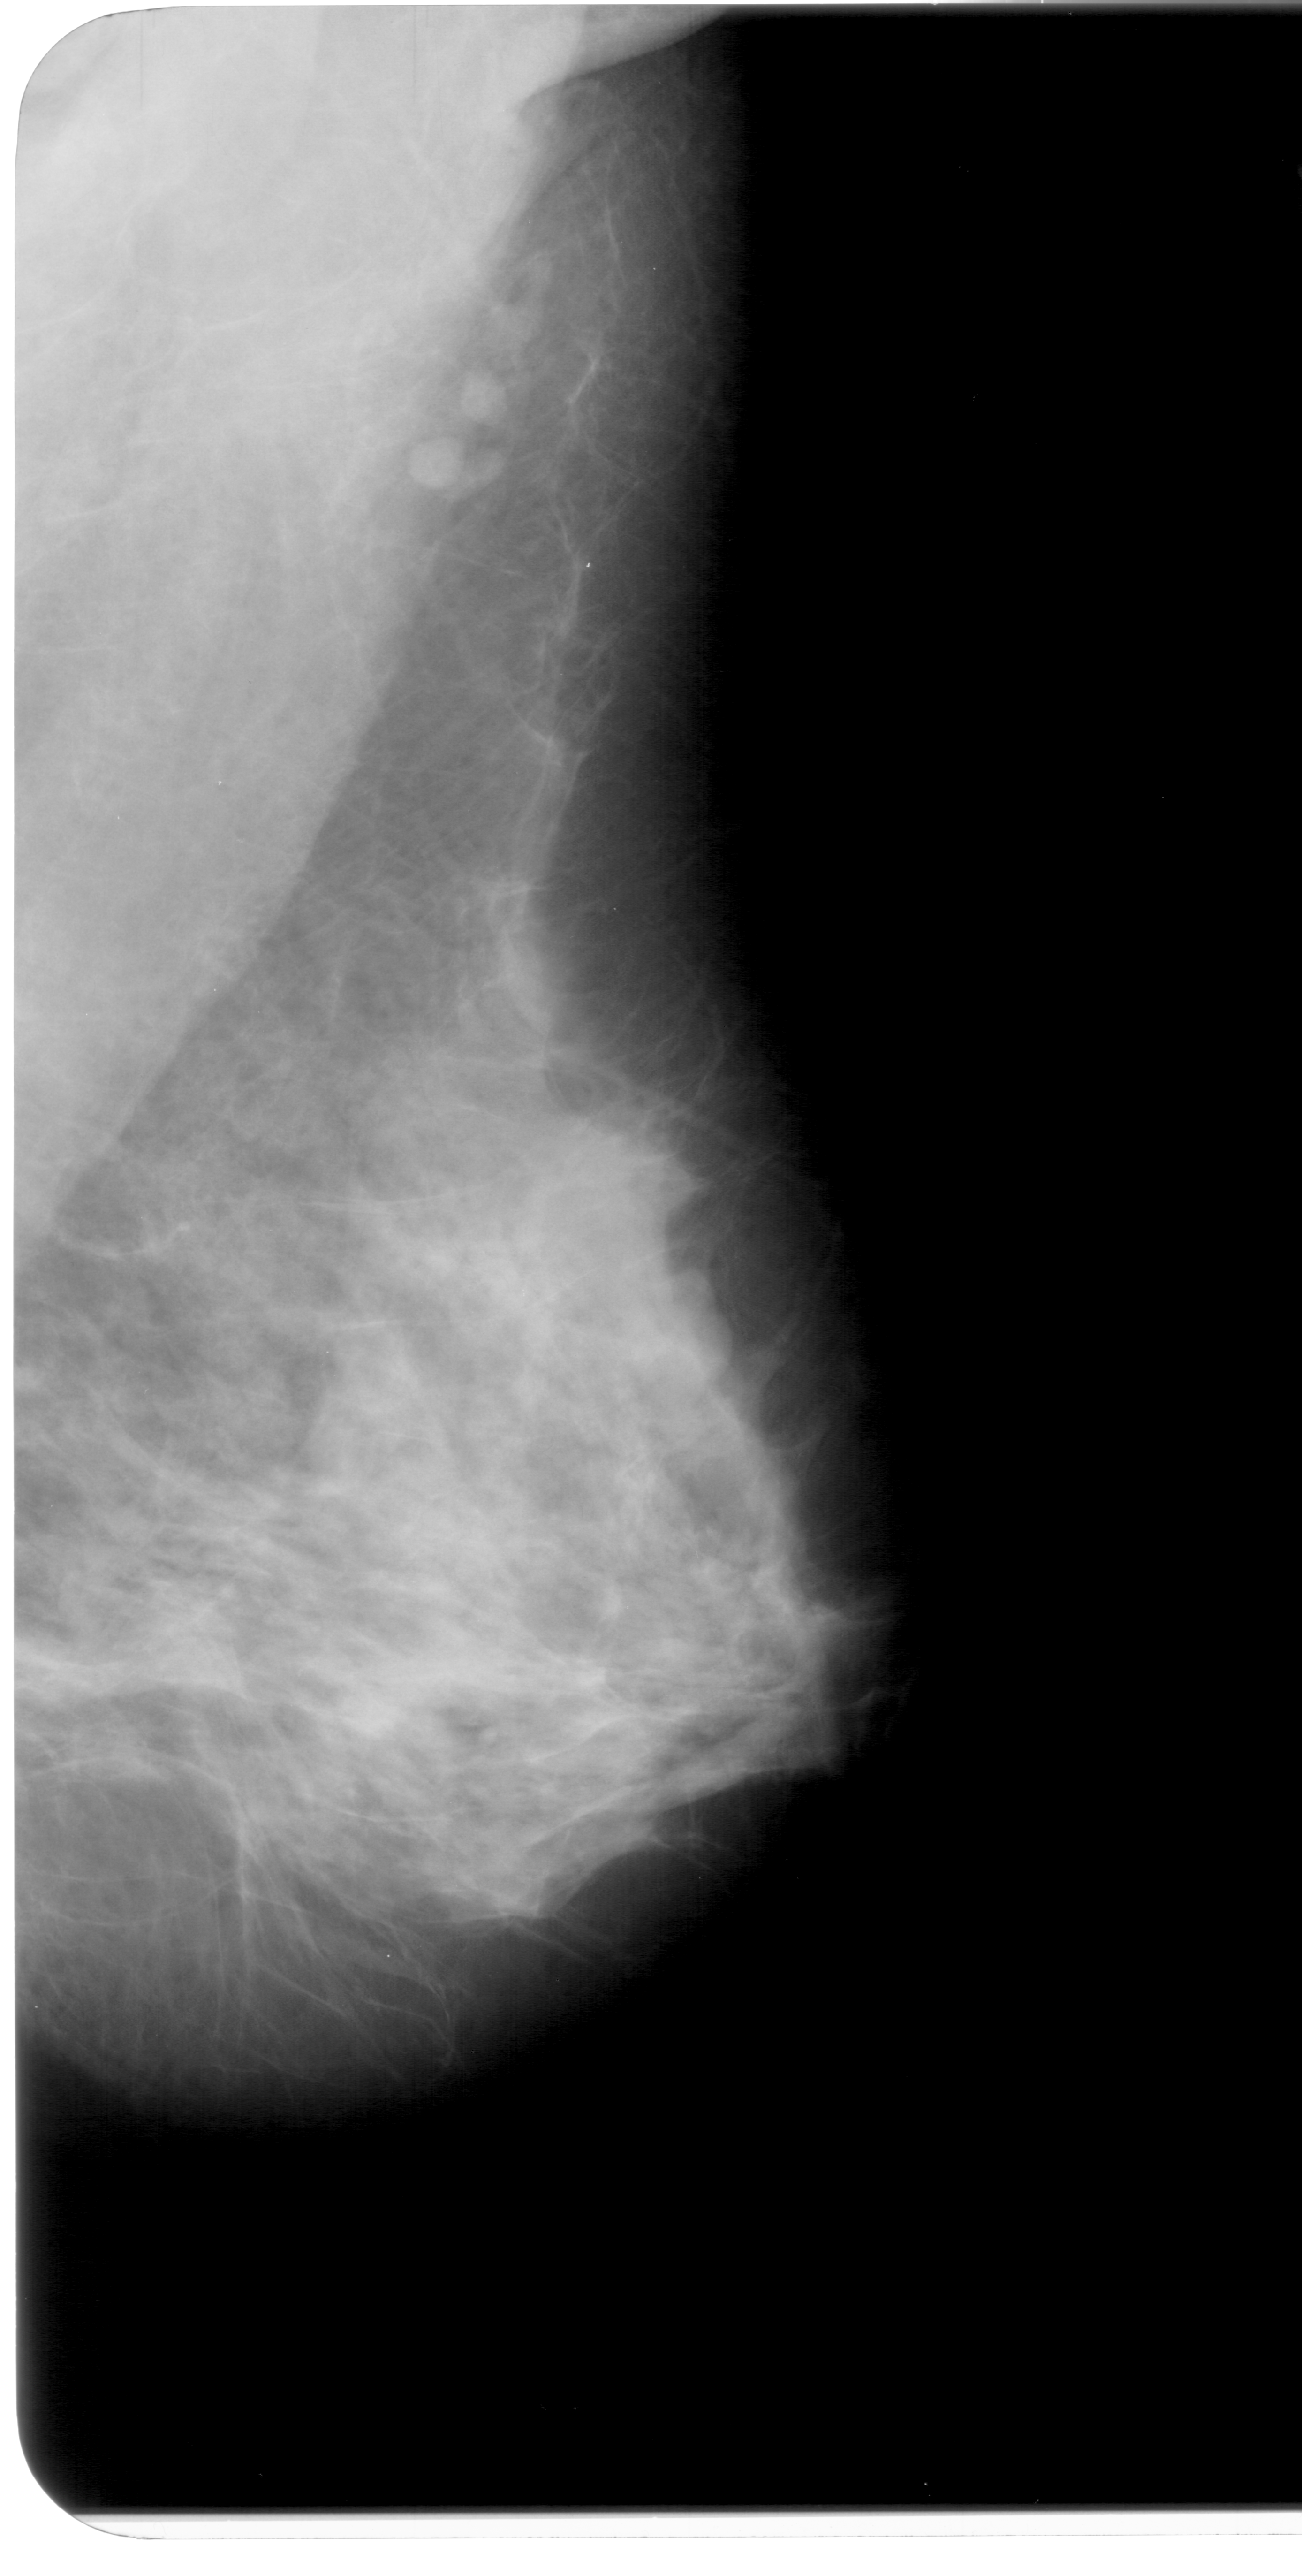
Mammogram (digitized film), right breast, mediolateral oblique (MLO) view, BI-RADS breast density category 3 (scale 1–4).
- Marked abnormality: mass, shape lobulated, margins obscured; BI-RADS assessment category 4; subtlety rating 2 on a 1 (subtle) to 5 (obvious) scale; pathology result (as recorded, not read from the image): benign.